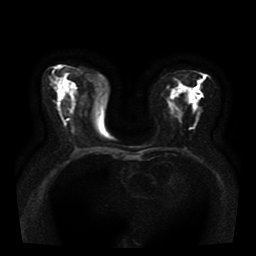
Breast MRI, one axial slice; position 19 of 41 along the scan axis; diffusion-weighted series; image 2 of 4 stored at this slice position (different b-values; order by instance number); 1.5 T; 256 × 256 image matrix. Female patient.
Annotated regions visible in this slice (expert manual segmentation):
- tumour on diffusion-weighted imaging: box from (x=192, y=90) to (x=202, y=100) px